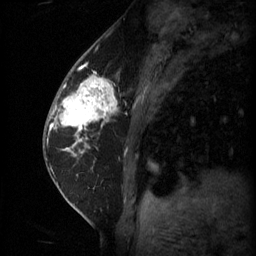
Breast MRI (dynamic contrast-enhanced), one sagittal slice; position 21 of 60 along the scan axis; 3 images stored at this slice position (order not interpretable as contrast timing); 1.5 T; TE 4.2 ms, TR 11 ms; 2 mm slice thickness; 256 × 256 image matrix, field of view 180 × 180 mm. Female patient, age 62 years.
Structures marked on this image (semi-automatic segmentation, software-assisted and operator-edited):
- analysis volume of interest (the breast-tissue region the enhancement analysis was run in; not a lesion): bounding box [x1, y1, x2, y2] px = [55, 72, 121, 135]
- tumour enhancement mask (voxels above the 70 % enhancement threshold inside the analysis volume of interest): [55, 76, 118, 133]